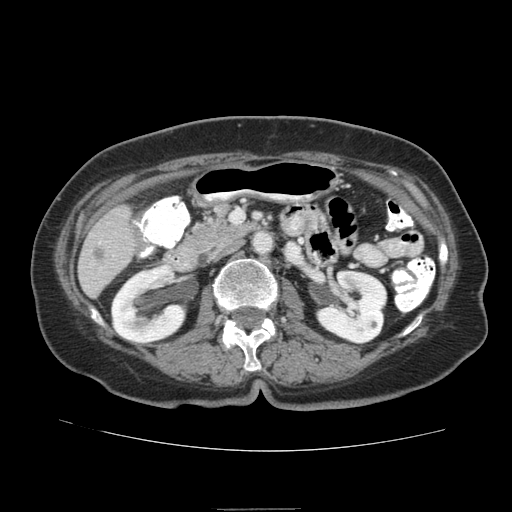
Contrast-enhanced abdominal CT (liver protocol), one axial slice; slice 29 of 95 in the series (ordered by position); reconstruction kernel STANDARD; 140 kVp; soft-tissue window (W 400 / L 40 HU); 512 × 512 image matrix. Case-level facts recorded for this patient, not image findings: diagnosis: hepatocellular carcinoma (patient treated with transarterial chemoembolisation; whether this scan precedes or follows treatment is not stated here); TNM stage (as recorded): Stage-IVA; Child-Pugh class: B; tumour differentiation: moderately differentiated; tumour nodularity: uninodular.
Annotated regions visible in this slice (semi-automatically segmented with operator editing):
- liver parenchyma outside the tumour (the mass and vessels are separate outlines, so this box may not span the whole liver): bounding box [x1, y1, x2, y2] px = [78, 204, 136, 298]